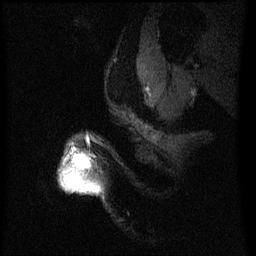
Breast MRI (dynamic contrast-enhanced), one sagittal slice. Slice 51 of 60 in the series (ordered by position). Dynamic contrast-enhanced series, image 2 of 3 at this slice position (ordered by acquisition). 1.5 T. TE 4.2 ms, TR 8 ms. 2.2 mm slice thickness. 256 × 256 image matrix, field of view 200 × 200 mm. Female patient, age 50 years.
Outlined on this slice (semi-automatic segmentation, software-assisted and operator-edited):
- analysis volume of interest (the breast-tissue region the enhancement analysis was run in; not a lesion): bounding box (x1, y1, x2, y2) in pixels: (69, 158, 84, 189)
- tumour enhancement mask (voxels above the 70 % enhancement threshold inside the analysis volume of interest): (70, 158, 84, 189)